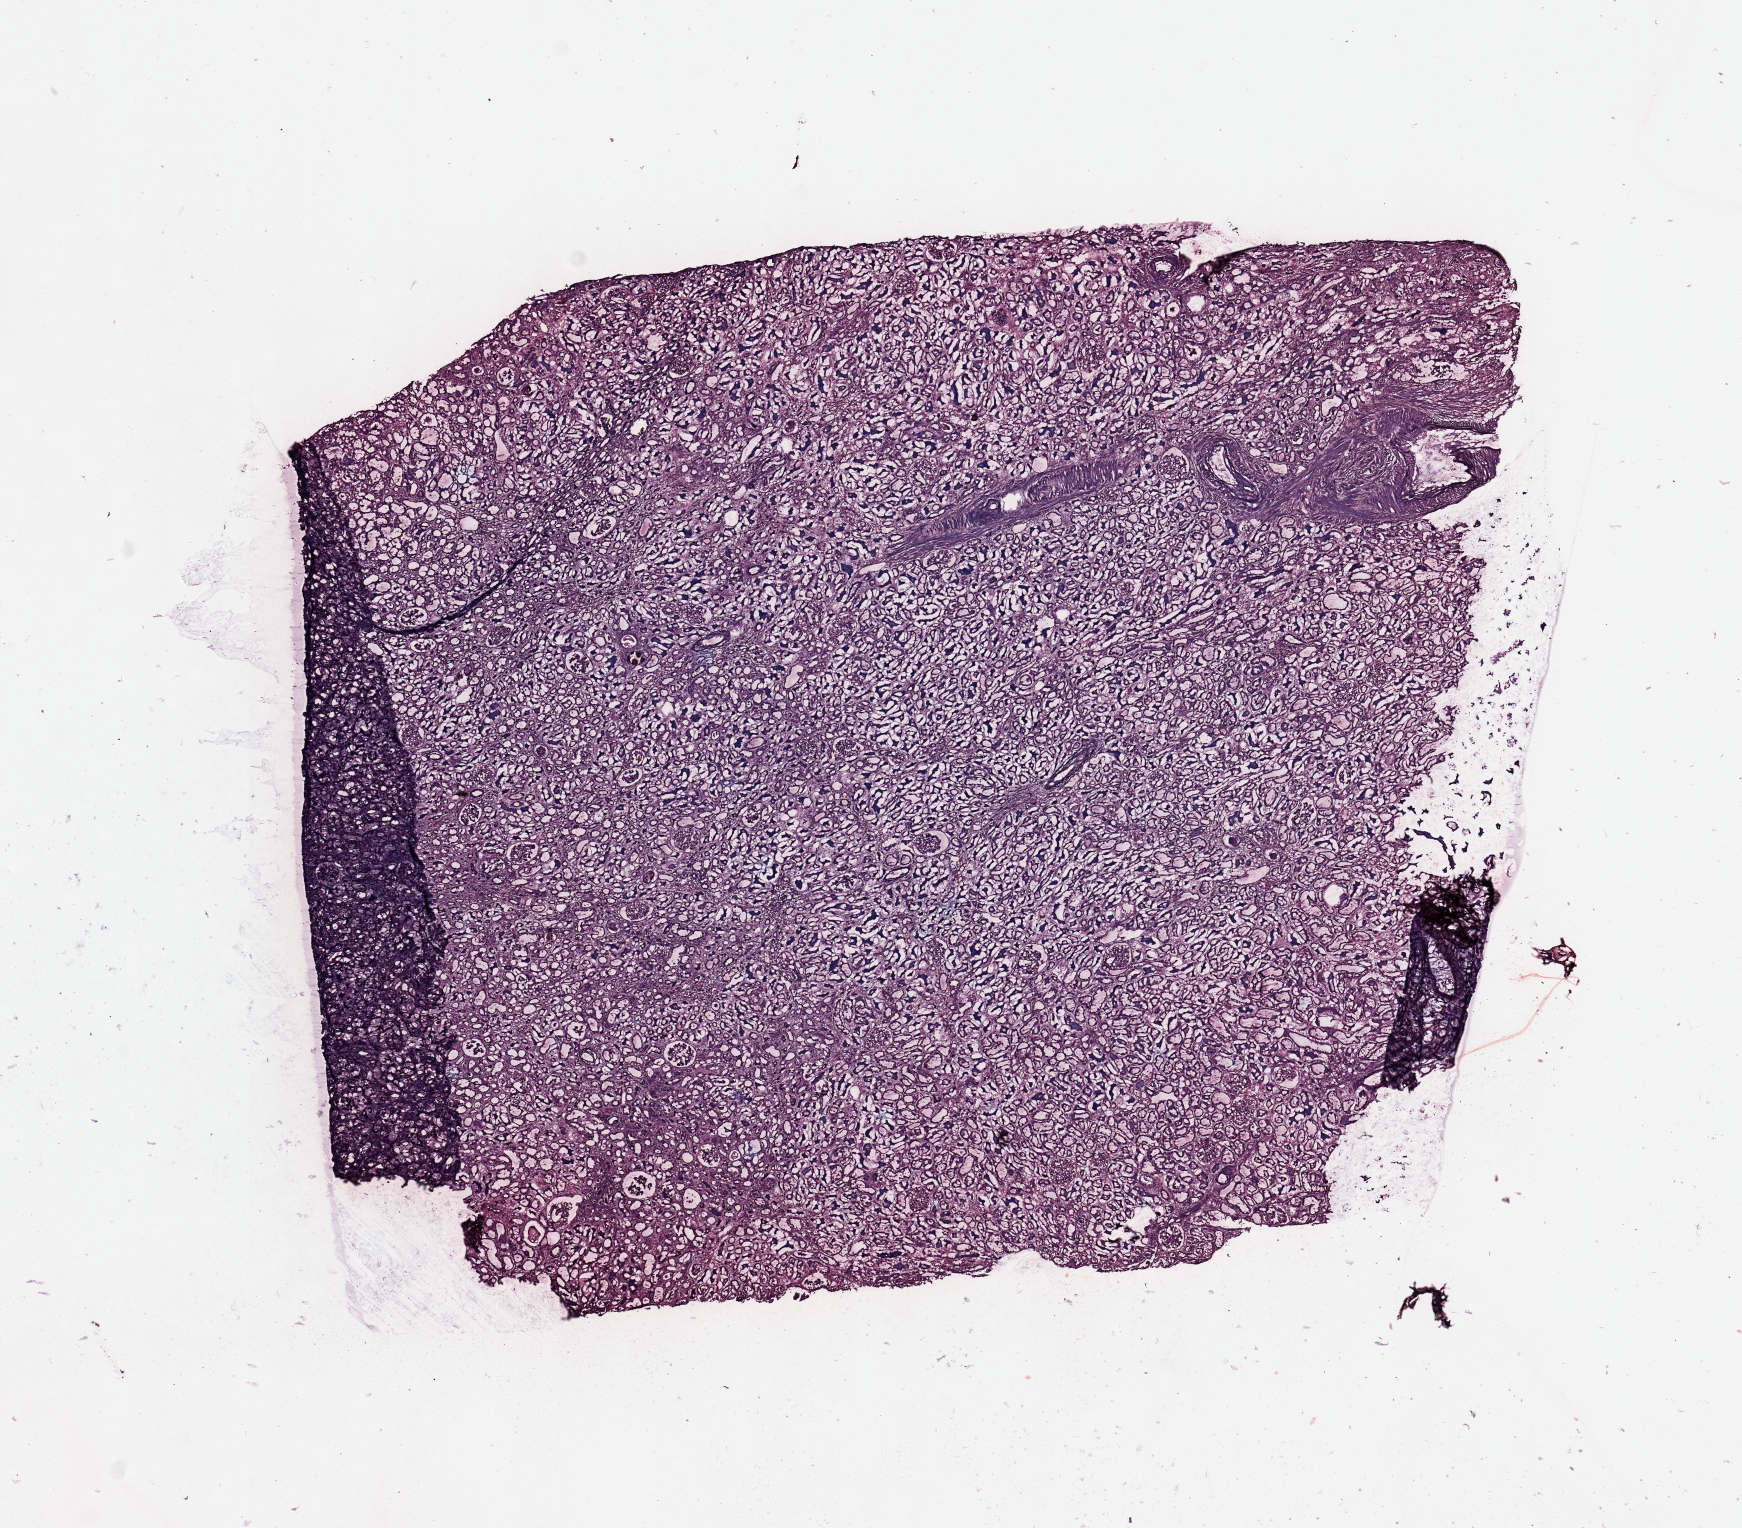
Digitized H&E tissue section (whole slide), a low-resolution overview of the entire scanned area, about 13.8 x 12.1 mm, normal (non-tumour) tissue sample, kidney. Male, 72 y/o.
- this section: normal (non-tumour) tissue from the same patient
- patient diagnosis: Renal cell carcinoma, NOS